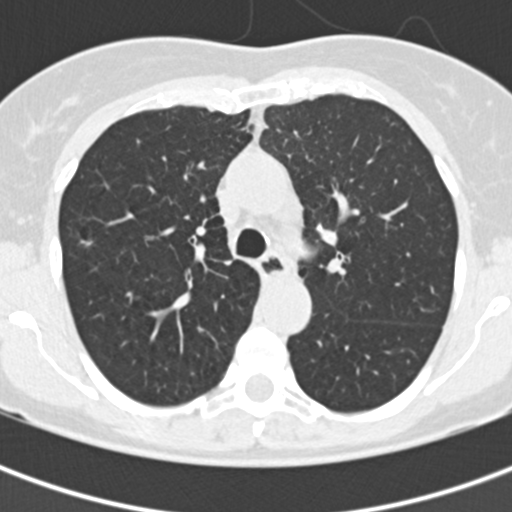
Chest CT (low-dose screening protocol), one axial image; baseline screening round; lung window (W 1500 / L -600 HU); 2 mm slice thickness; 120 kVp; slice 63 of 177 in the series; 512 × 512 image matrix, field of view 280 × 280 mm. Female participant, aged 60 years at enrolment. Current smoker at enrolment.
Lesion marked by an expert reader, bounding box <60,221,110,269> (left, top, right, bottom; pixels). No non-calcified nodule or mass ≥4 mm was recorded by the screening reader at this exam. Official screen result: negative screen, no significant abnormalities. Lung cancer was diagnosed 861 days after this screen (after the third annual screen): bronchiolo-alveolar adenocarcinoma, NOS, right upper lobe, well differentiated (G1), stage IA (AJCC 6th edition), 11 mm at pathology.